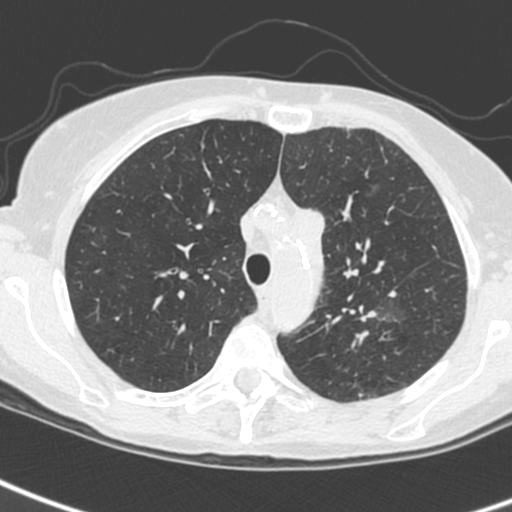
Chest CT (low-dose screening protocol), one axial image; baseline annual screen; lung window (W 1500 / L -600 HU); slice 55 of 242 in the series. Female participant, aged 61 years at enrolment. Current smoker at enrolment.
• Lesion marked by an expert reader, box from (x=341, y=287) to (x=411, y=346) px.
• The screening reader recorded 2 non-calcified nodules or masses ≥4 mm on this exam (left upper lobe, left upper lobe); which of them this box marks is not recorded.
• Later outcome: lung cancer diagnosed 29 days after this screen — small cell carcinoma, NOS, left upper lobe, stage IV (AJCC 6th edition).